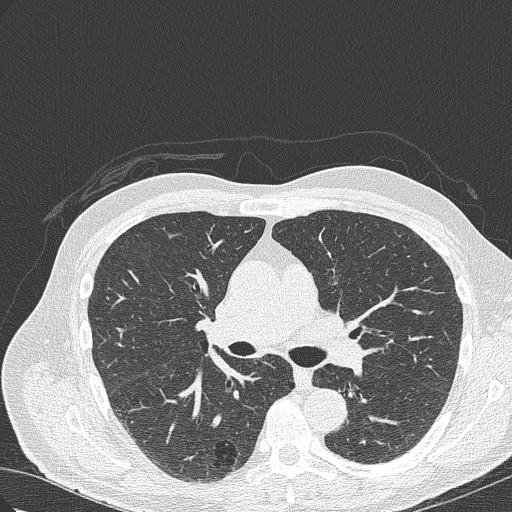
Chest CT (low-dose screening protocol), one axial image. Baseline annual screen. Lung window (W 1500 / L -600 HU). 1 mm slice thickness. 120 kVp. Slice 130 of 322 in the series. Male participant, aged 70 years at enrolment.
Expert-annotated lung lesion, bounding box (x1, y1, x2, y2) in pixels: (199, 419, 263, 473). The screening reader recorded 4 non-calcified nodules or masses ≥4 mm on this exam (right lower lobe, right lower lobe, right upper lobe, right lower lobe); which of them this box marks is not recorded. Official screen result: positive, change unspecified: nodule(s) >= 4 mm or enlarging nodule(s), mass(es), or other non-specific abnormalities suspicious for lung cancer.